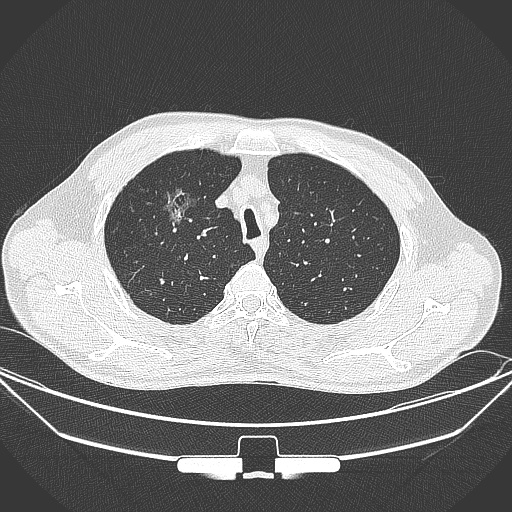
Chest CT, one axial slice; slice 279 of 355 in the series (ordered by position); lung window (W 1500 / L -600 HU); 512 × 512 image matrix, field of view 399 × 399 mm. Male patient, age 67 years. From the clinical record (not read from this slice): clinical TNM (as recorded): T1c N0 M0.
Structures marked on this image (bounding box drawn by a radiologist):
- lung tumour (recorded histology: adenocarcinoma): bounding box <161,179,193,230> (left, top, right, bottom; pixels)